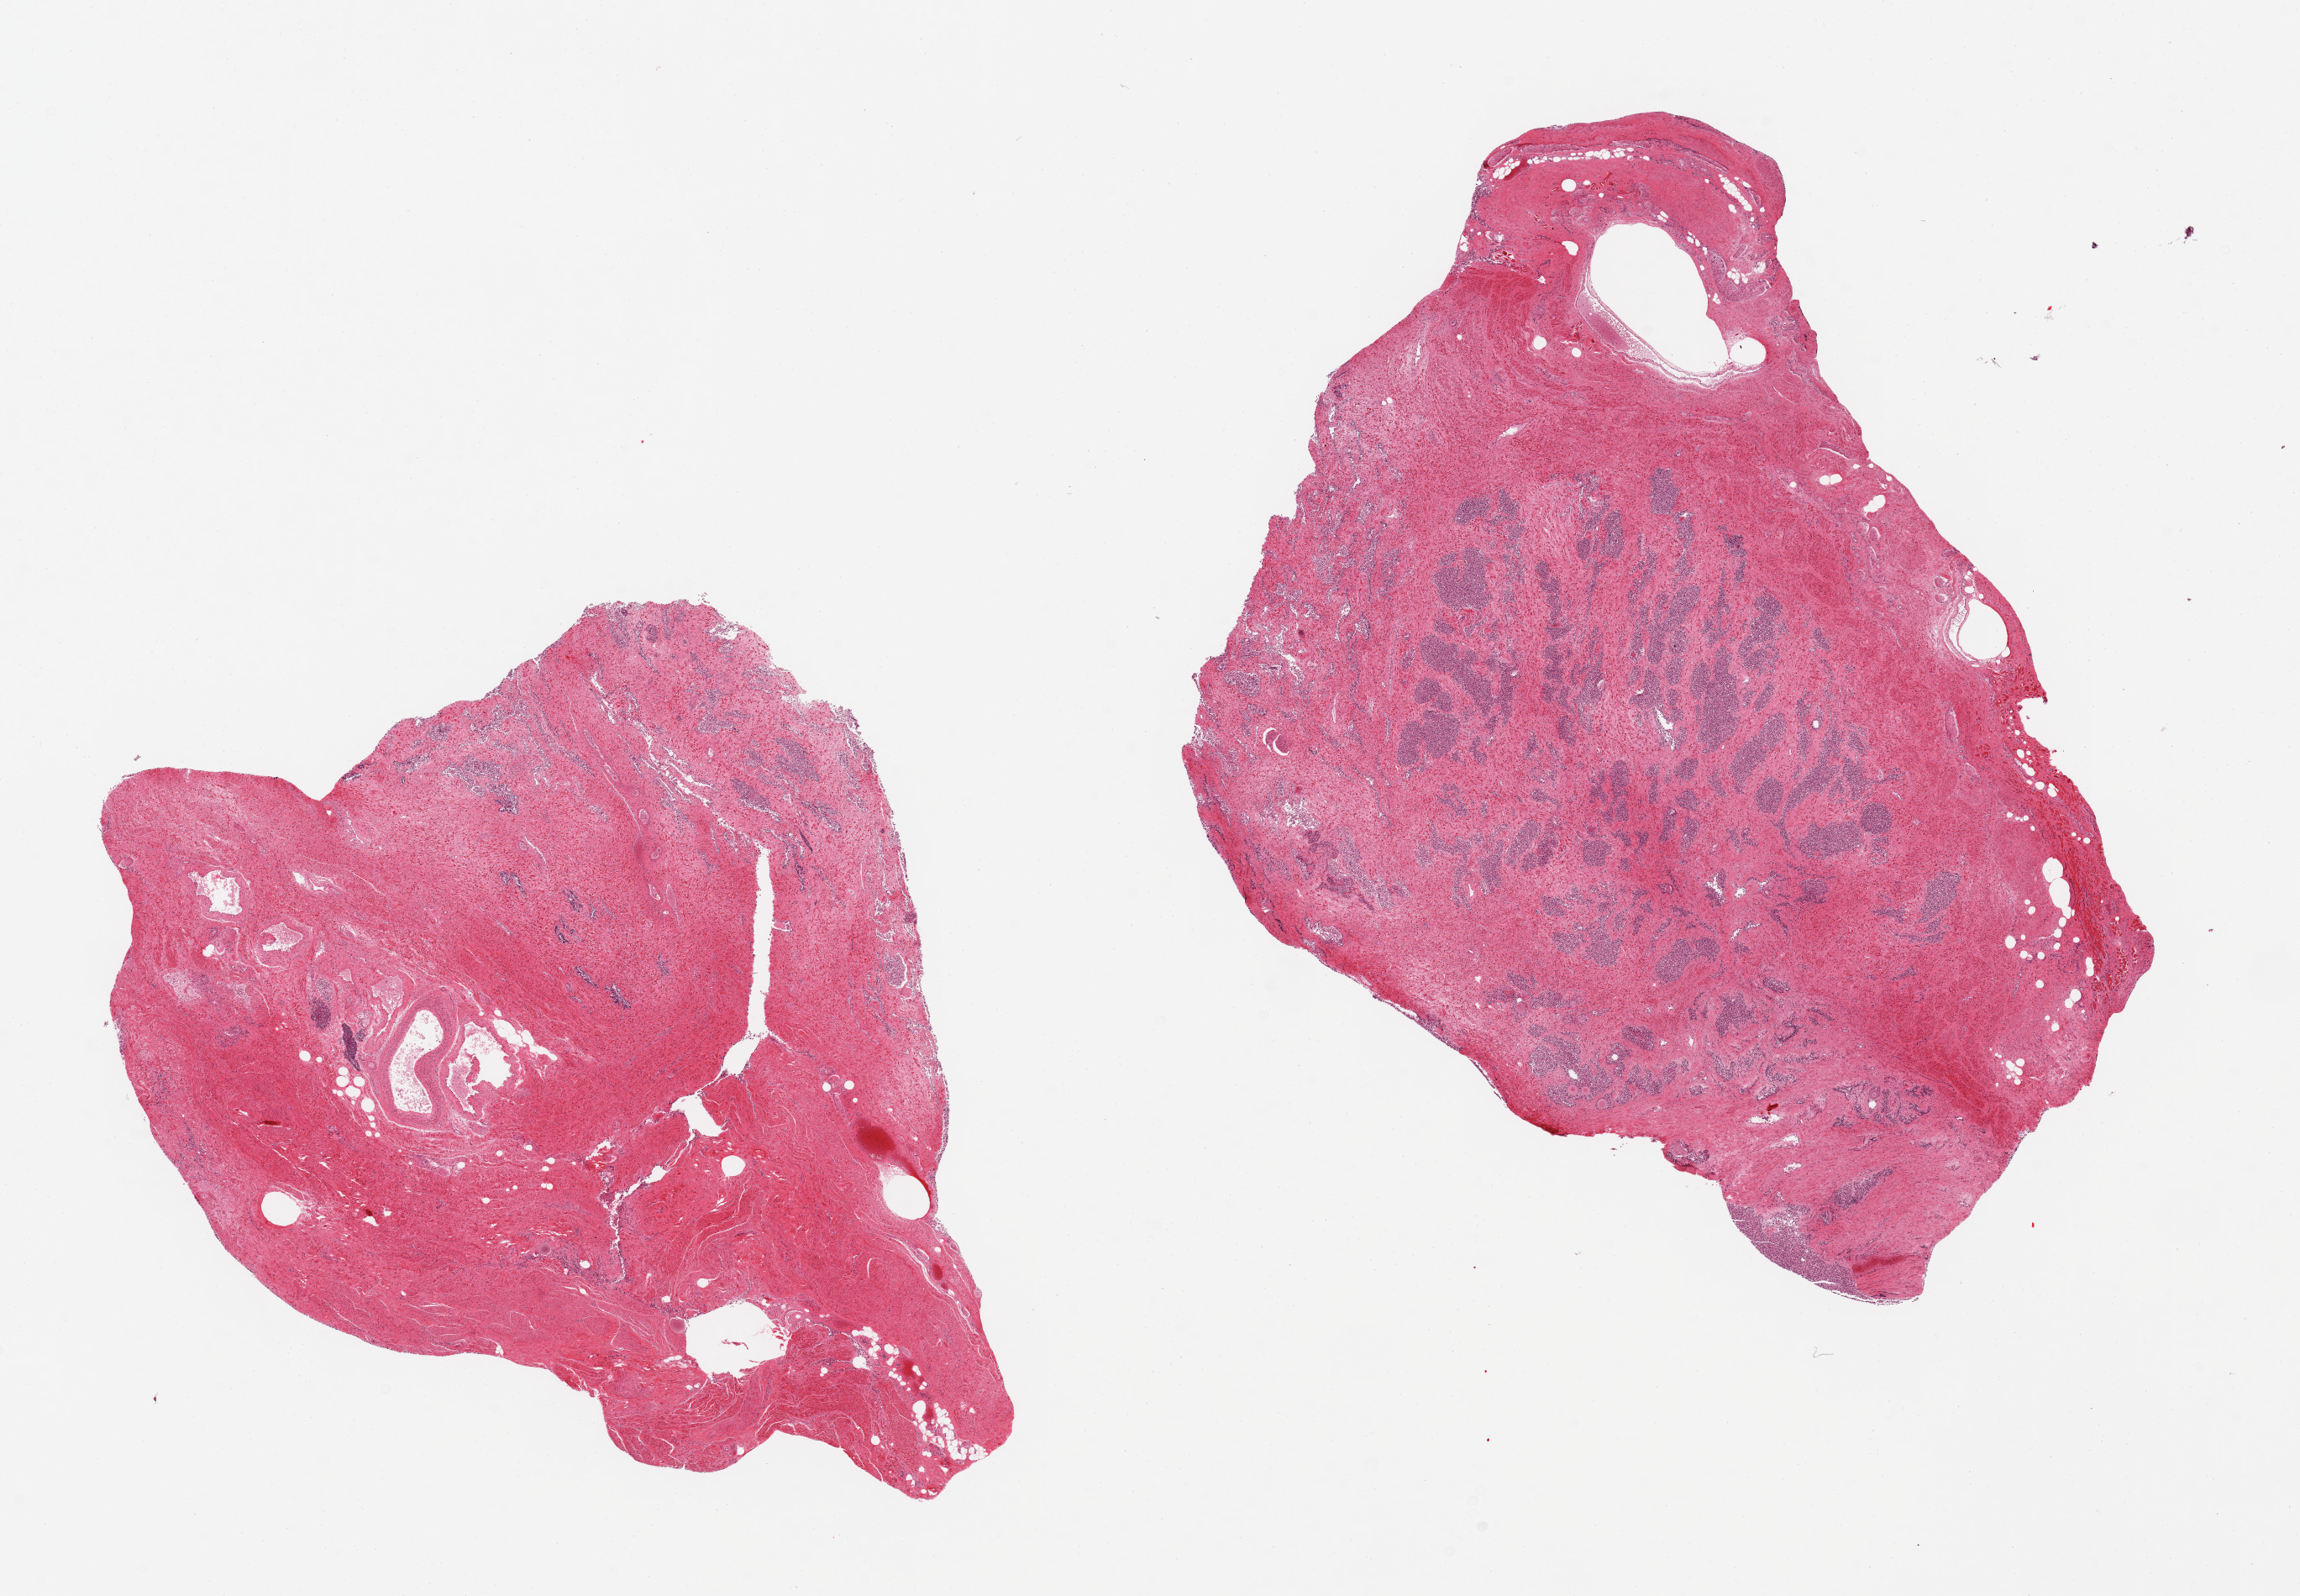
Whole-slide image, hematoxylin and eosin (H&E) stain — a low-resolution overview of the entire scanned area, about 21.7 x 15.0 mm, PAXgene-fixed, paraffin-embedded tissue, sampled site (target tissue): prostate, donor tissue sample.
- reviewer comment on this tissue sample: 2 pieces, glandular elements totally autolzyed, hyperplastic pattern